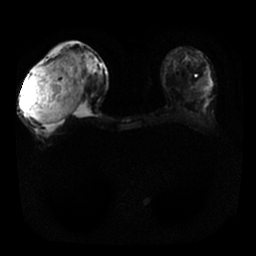
Breast MRI, one axial slice; position 6 of 25 along the scan axis; diffusion-weighted series; image 2 of 4 stored at this slice position (different b-values; order by instance number); 1.5 T; 4 mm slice thickness; 256 × 256 image matrix. Female patient.
Outlined on this slice (outlined manually by an expert reader):
- tumour on diffusion-weighted imaging: bounding box (x1, y1, x2, y2) in pixels: (21, 52, 86, 124)